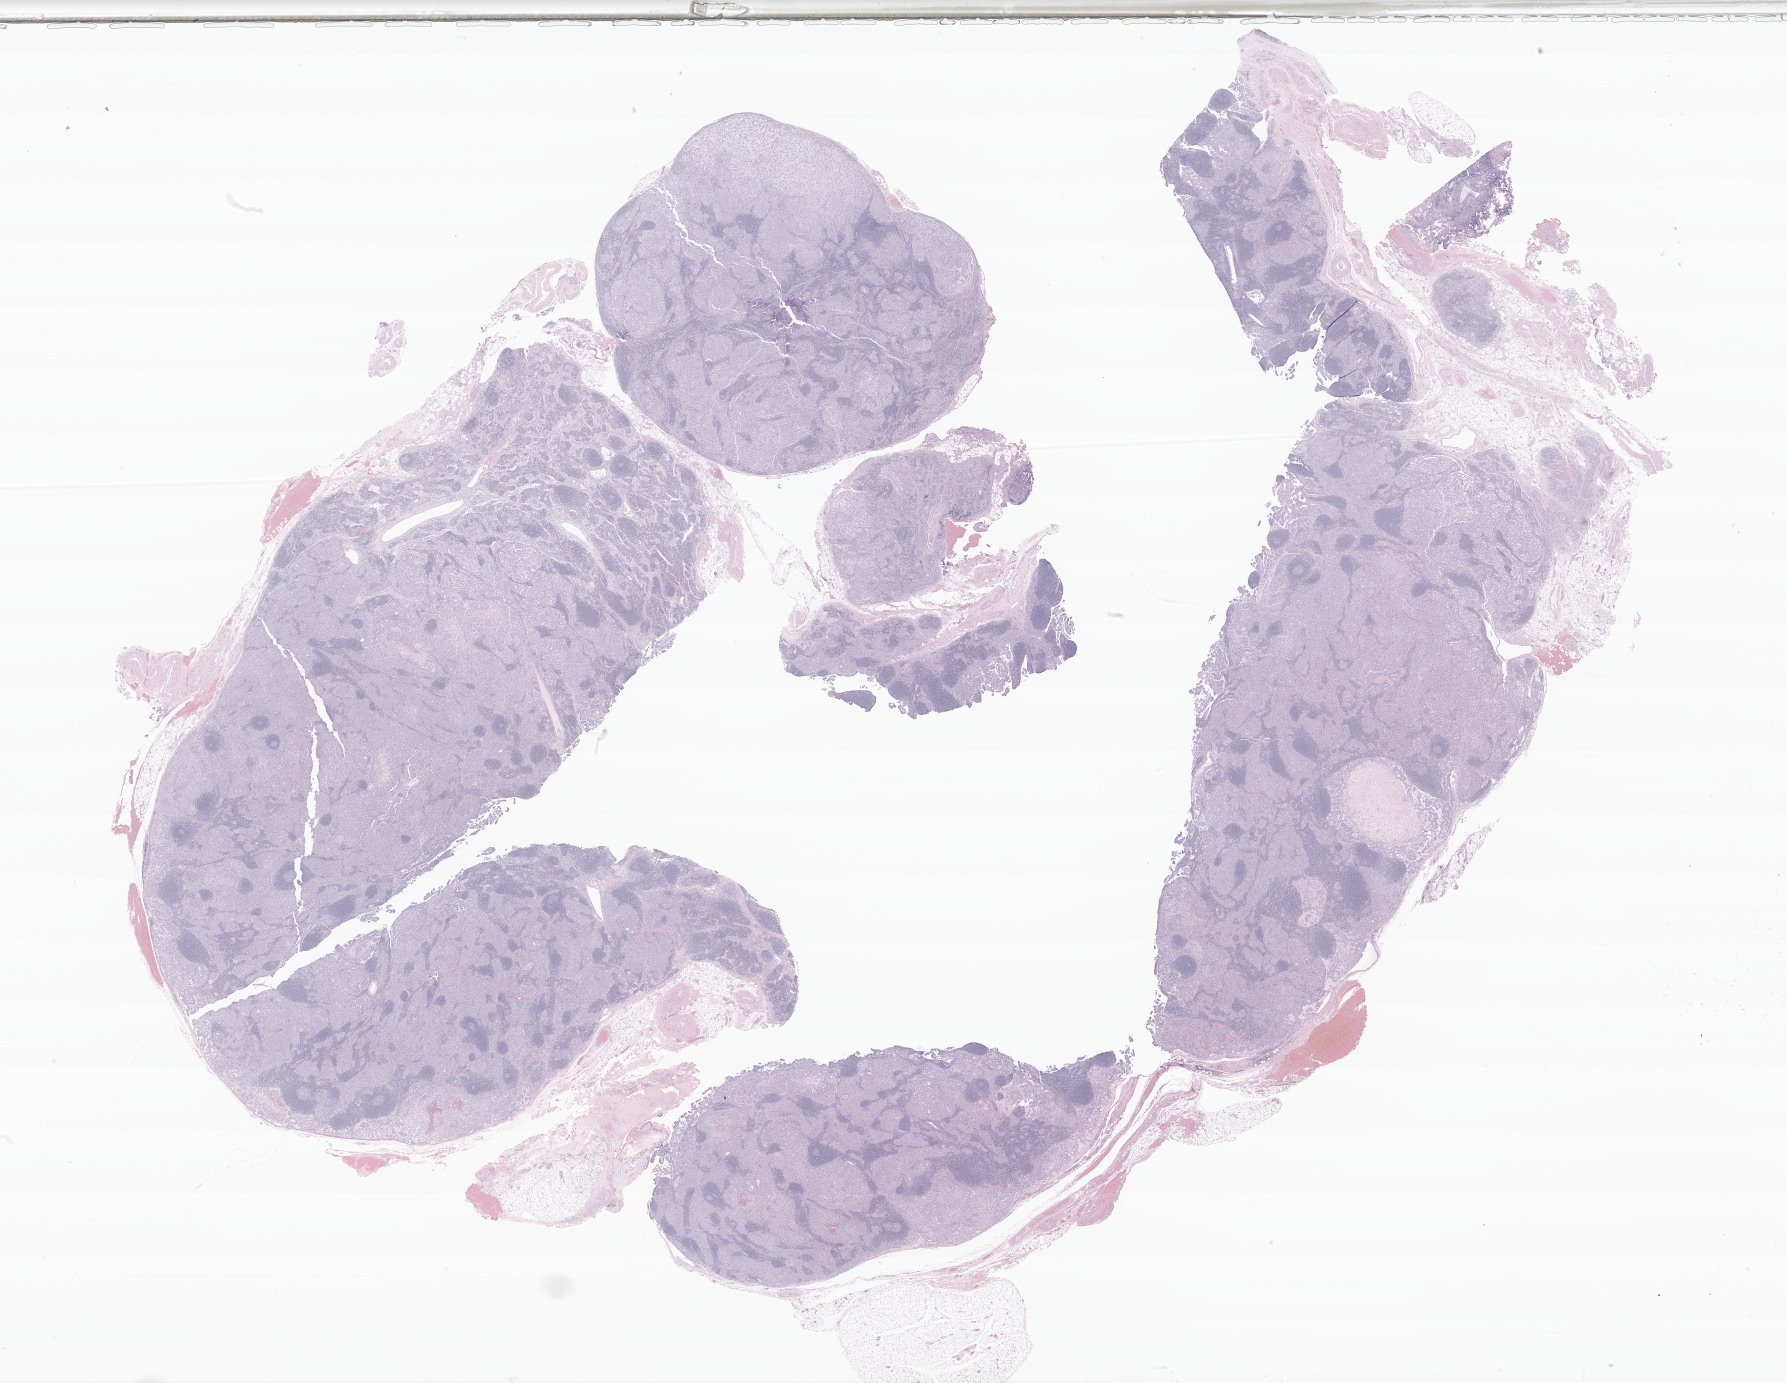
Whole-slide image, haematoxylin and eosin stain of tumor tissue from the kidney, shown as a low-resolution overview of the whole scanned area (about 30.1 x 23.3 mm), FFPE section. Female patient, age 186 months (15 years 6 months).
Diagnosis (ICD-O-3 morphology term): Medullary carcinoma, NOS.